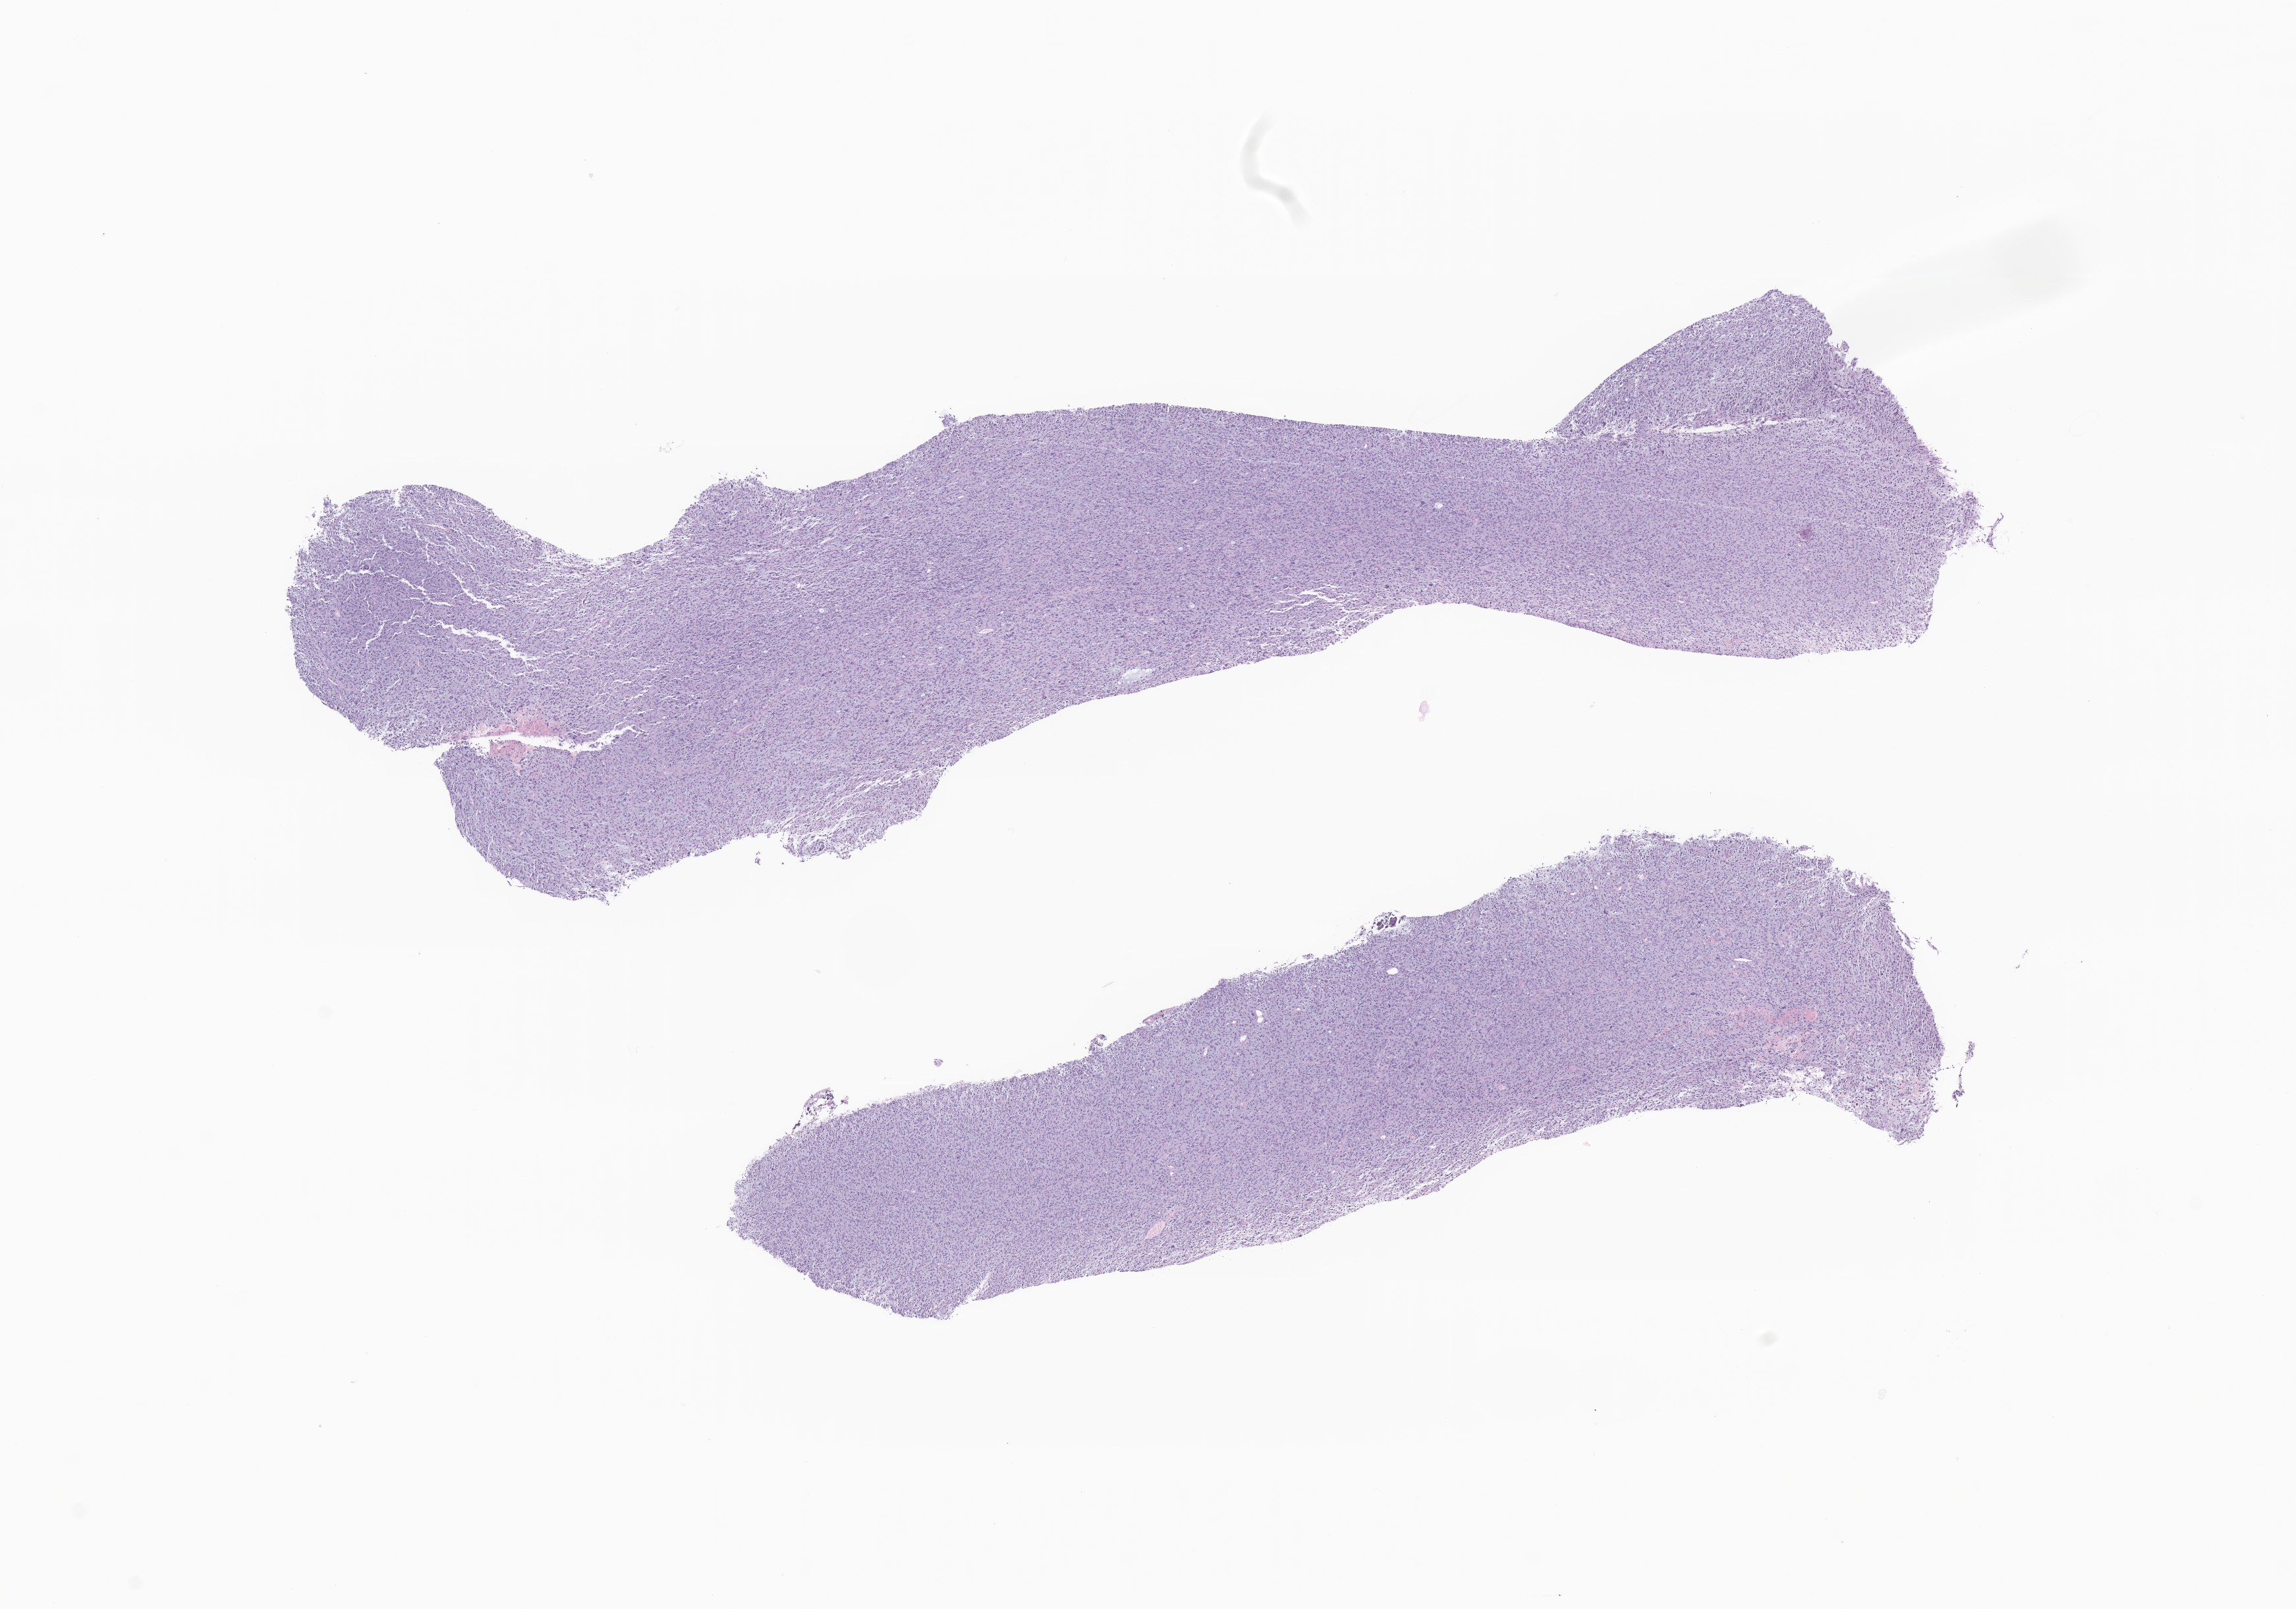
Whole-slide image, hematoxylin and eosin (H&E) stain of tumor tissue from the brain — a low-resolution overview of the entire scanned area, about 14.7 x 10.3 mm; formalin-fixed, paraffin-embedded (FFPE) tissue. Patient male; age 138 months (11 years 6 months).
Diagnosis (ICD-O-3 morphology term): Glioma, malignant.